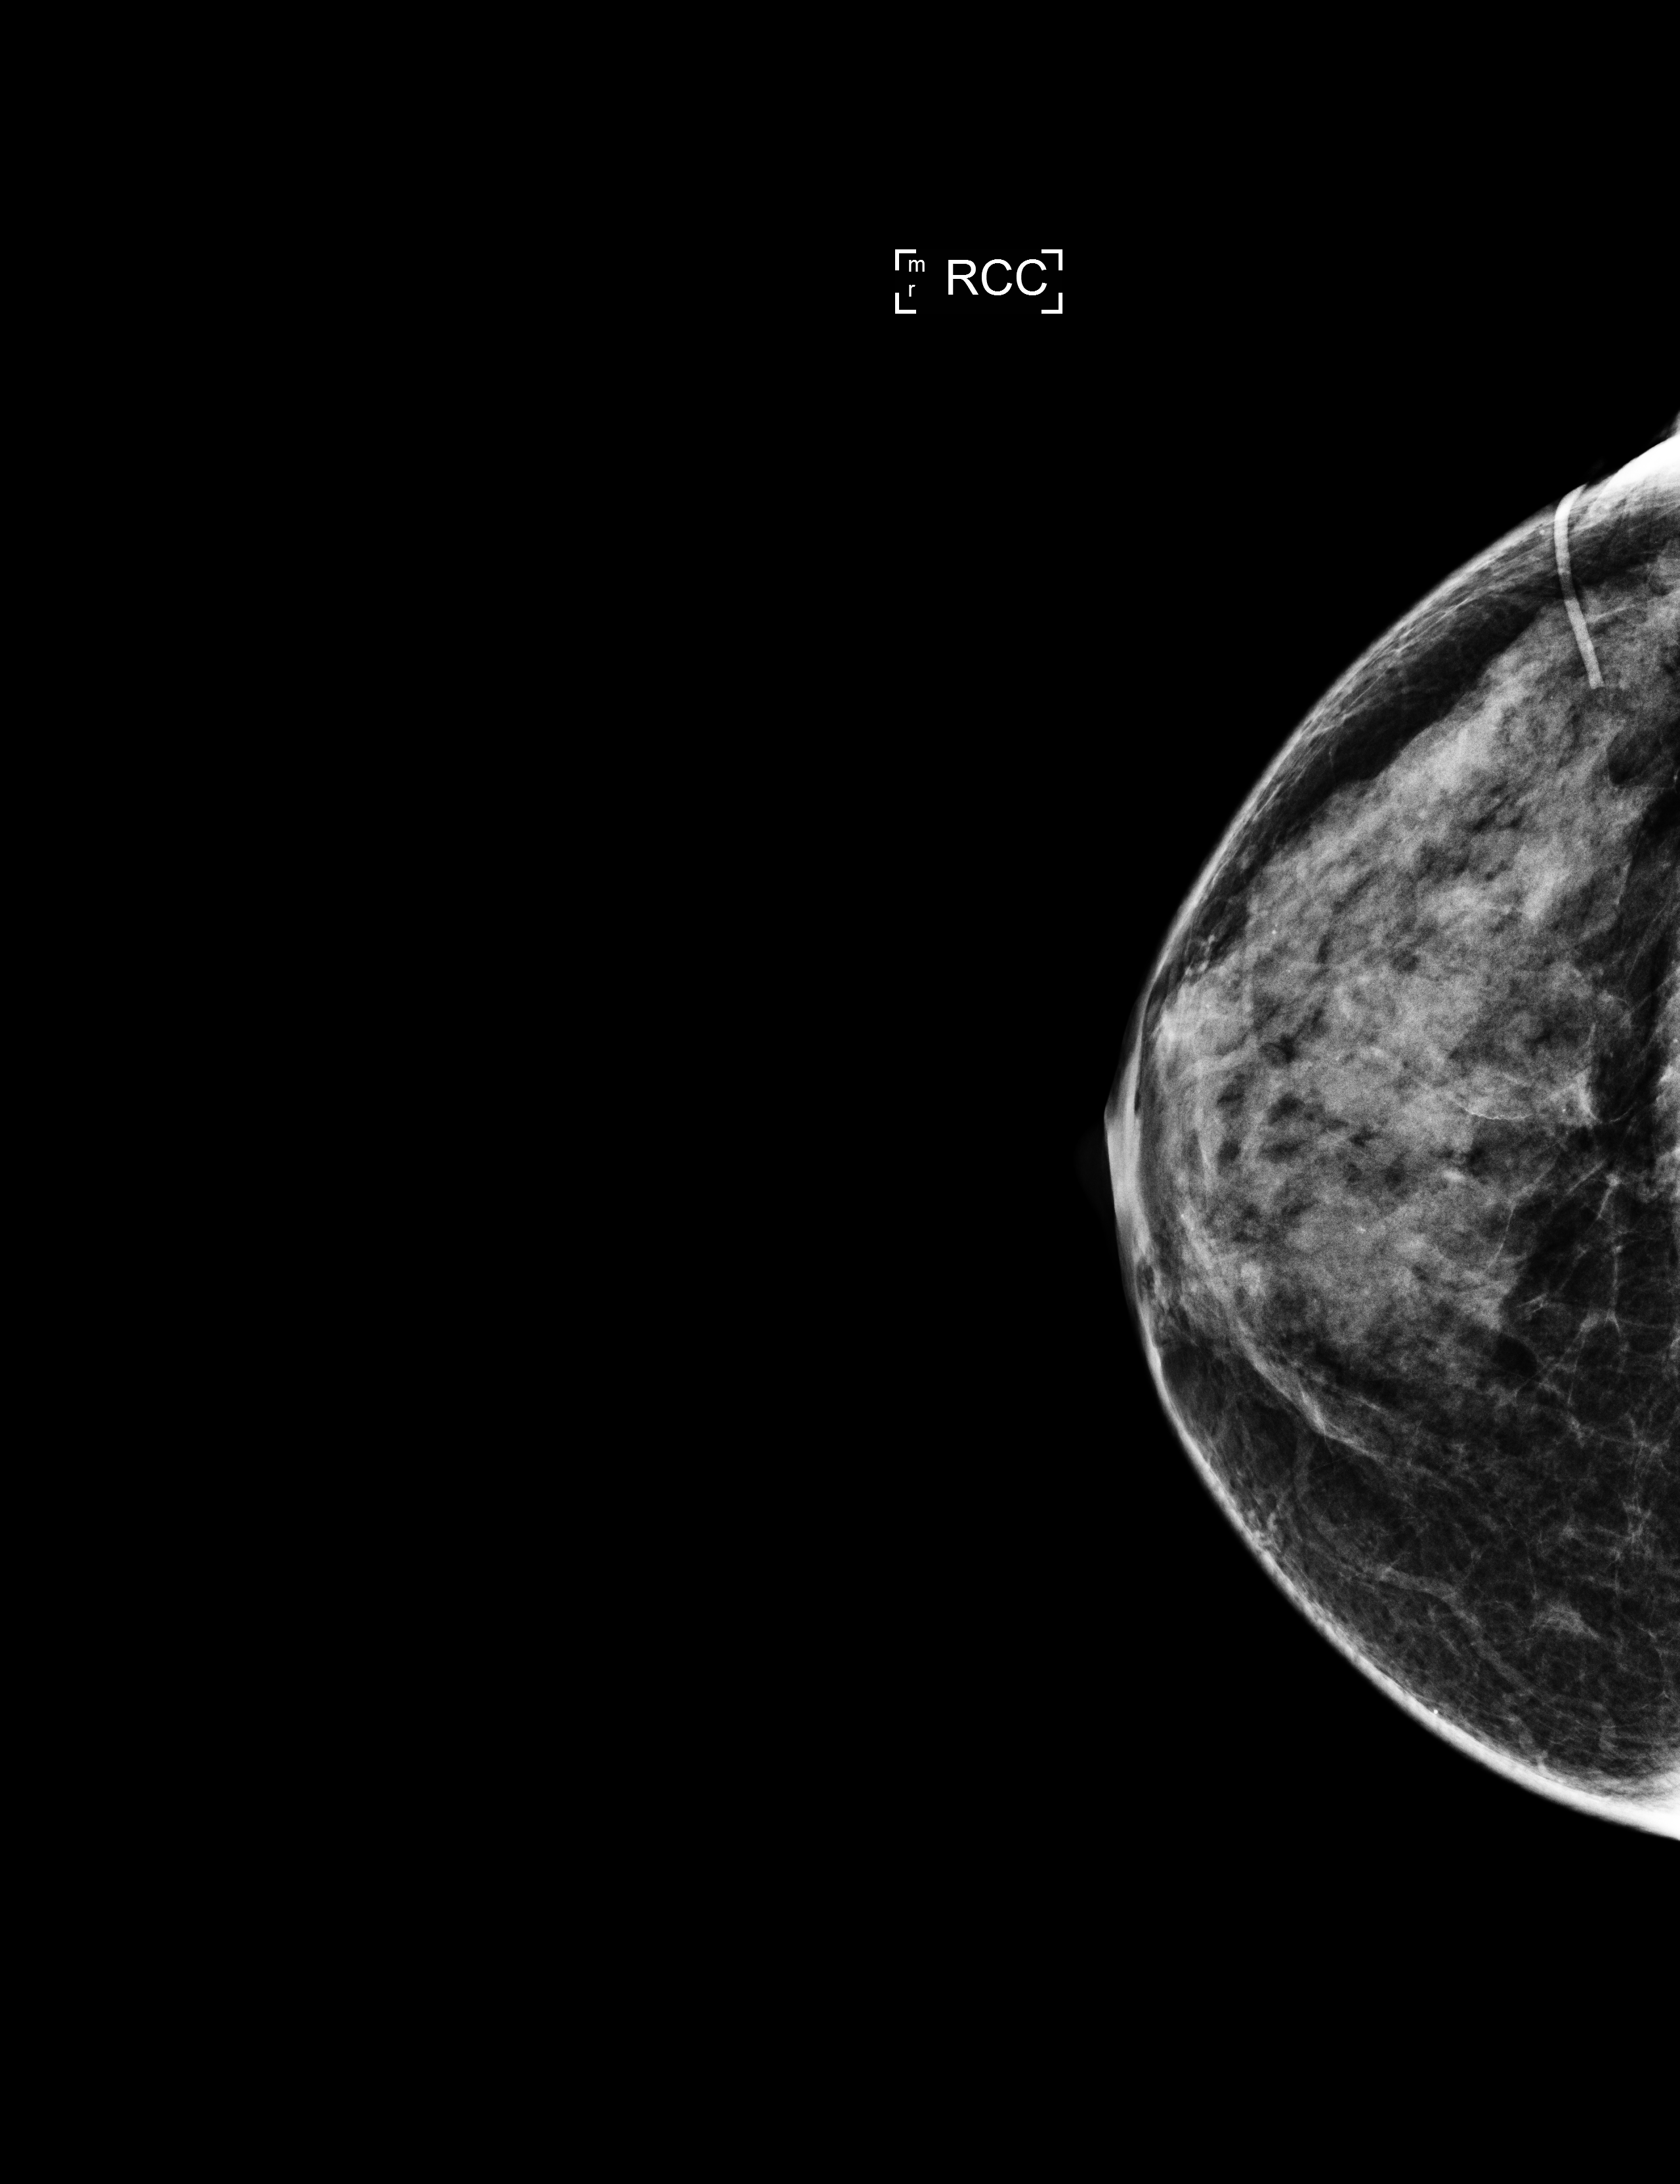
Annual screening mammography examination. Patient: female, 51 years.
Image type: full-field digital mammogram. Breast: right. Projection: craniocaudal (CC) view.